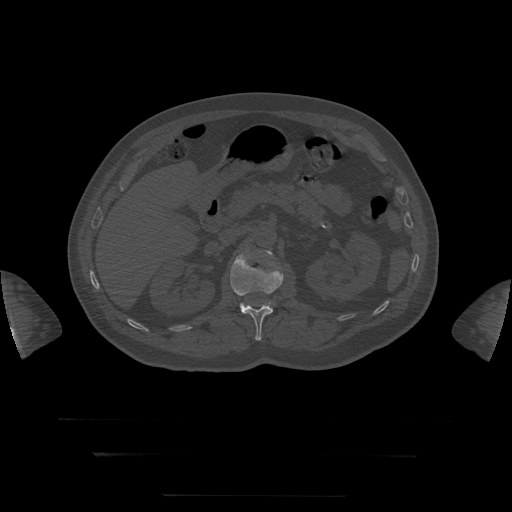
CT including the spine, one axial slice. Position 43 of 397 along the scan axis. 120 kVp. Bone window (W 1800 / L 400 HU). 1.25 mm slice thickness. 512 × 512 image matrix. Patient age 73 years. From the clinical record (not read from this slice): primary cancer: prostate.
Annotated regions visible in this slice (semi-automatically segmented with operator editing):
- L1 vertebra: box from (x=231, y=250) to (x=284, y=341) px